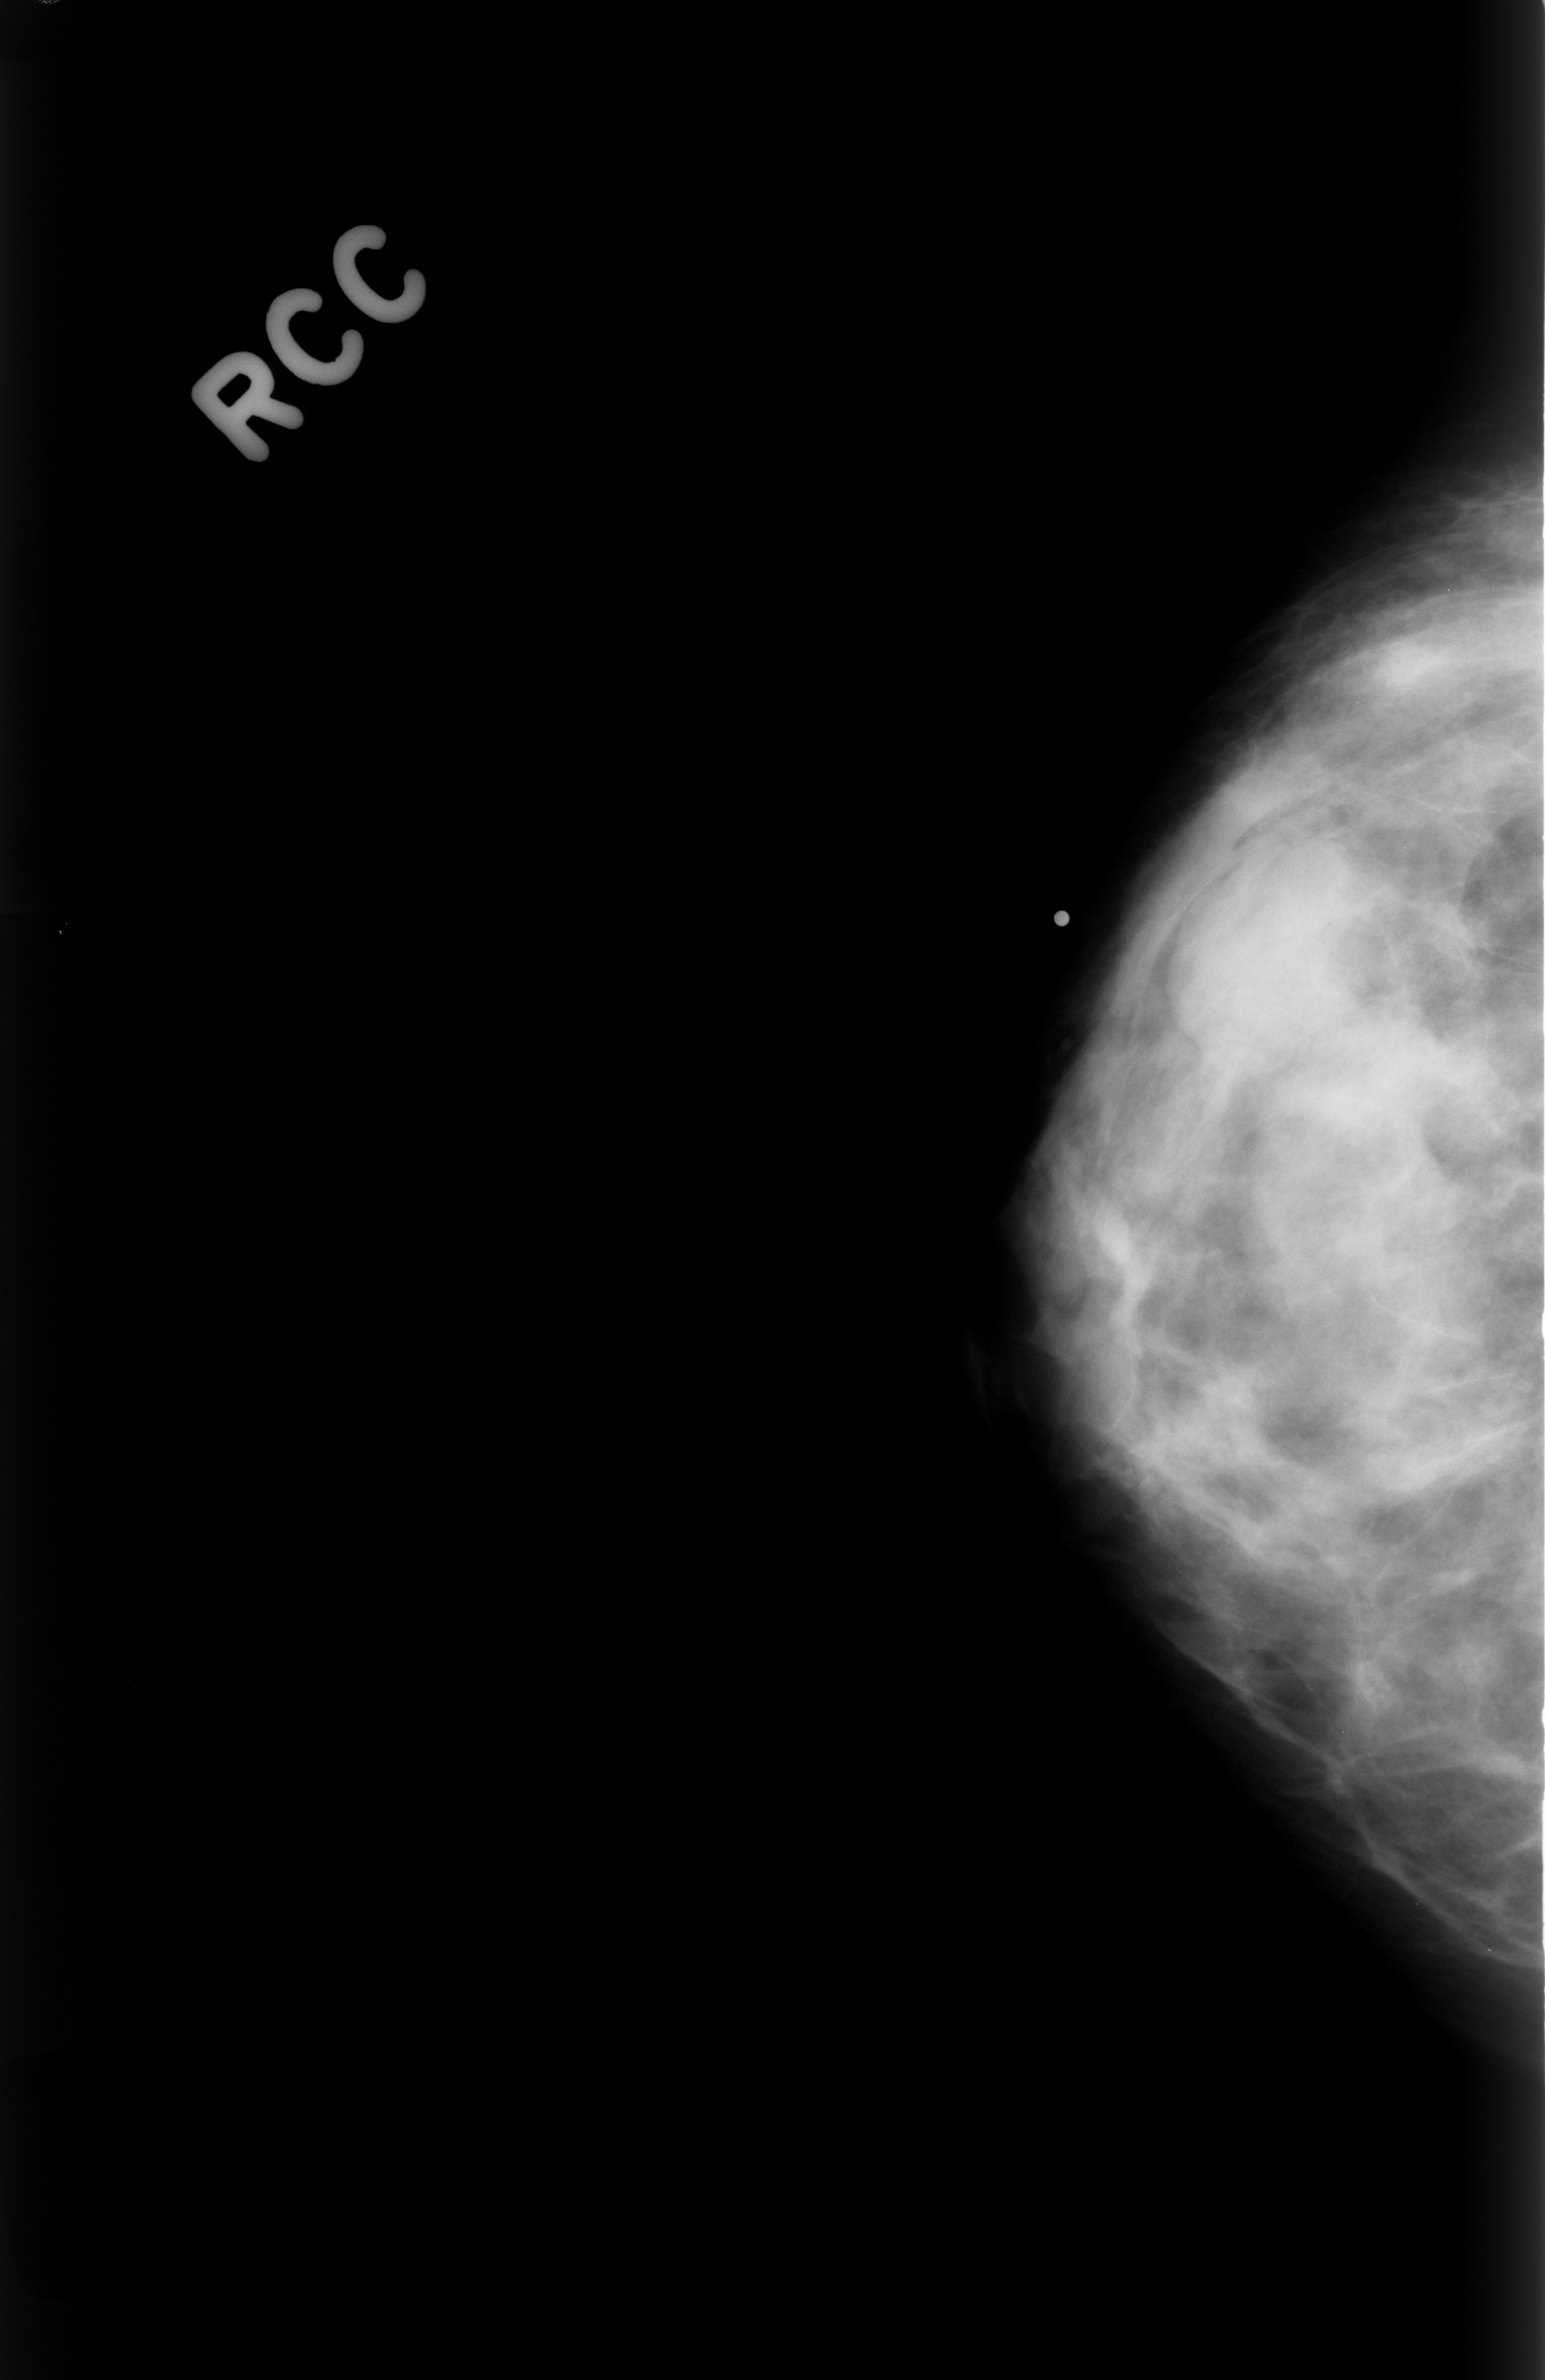
Digitized screen-film mammogram, right breast, CC view, breast composition: heterogeneously dense (BI-RADS density category 3 of 4).
Marked abnormality: mass, shape oval, margins obscured; BI-RADS assessment category 3; subtlety rating 4 on a 1 (subtle) to 5 (obvious) scale; pathology result (as recorded, not read from the image): benign.